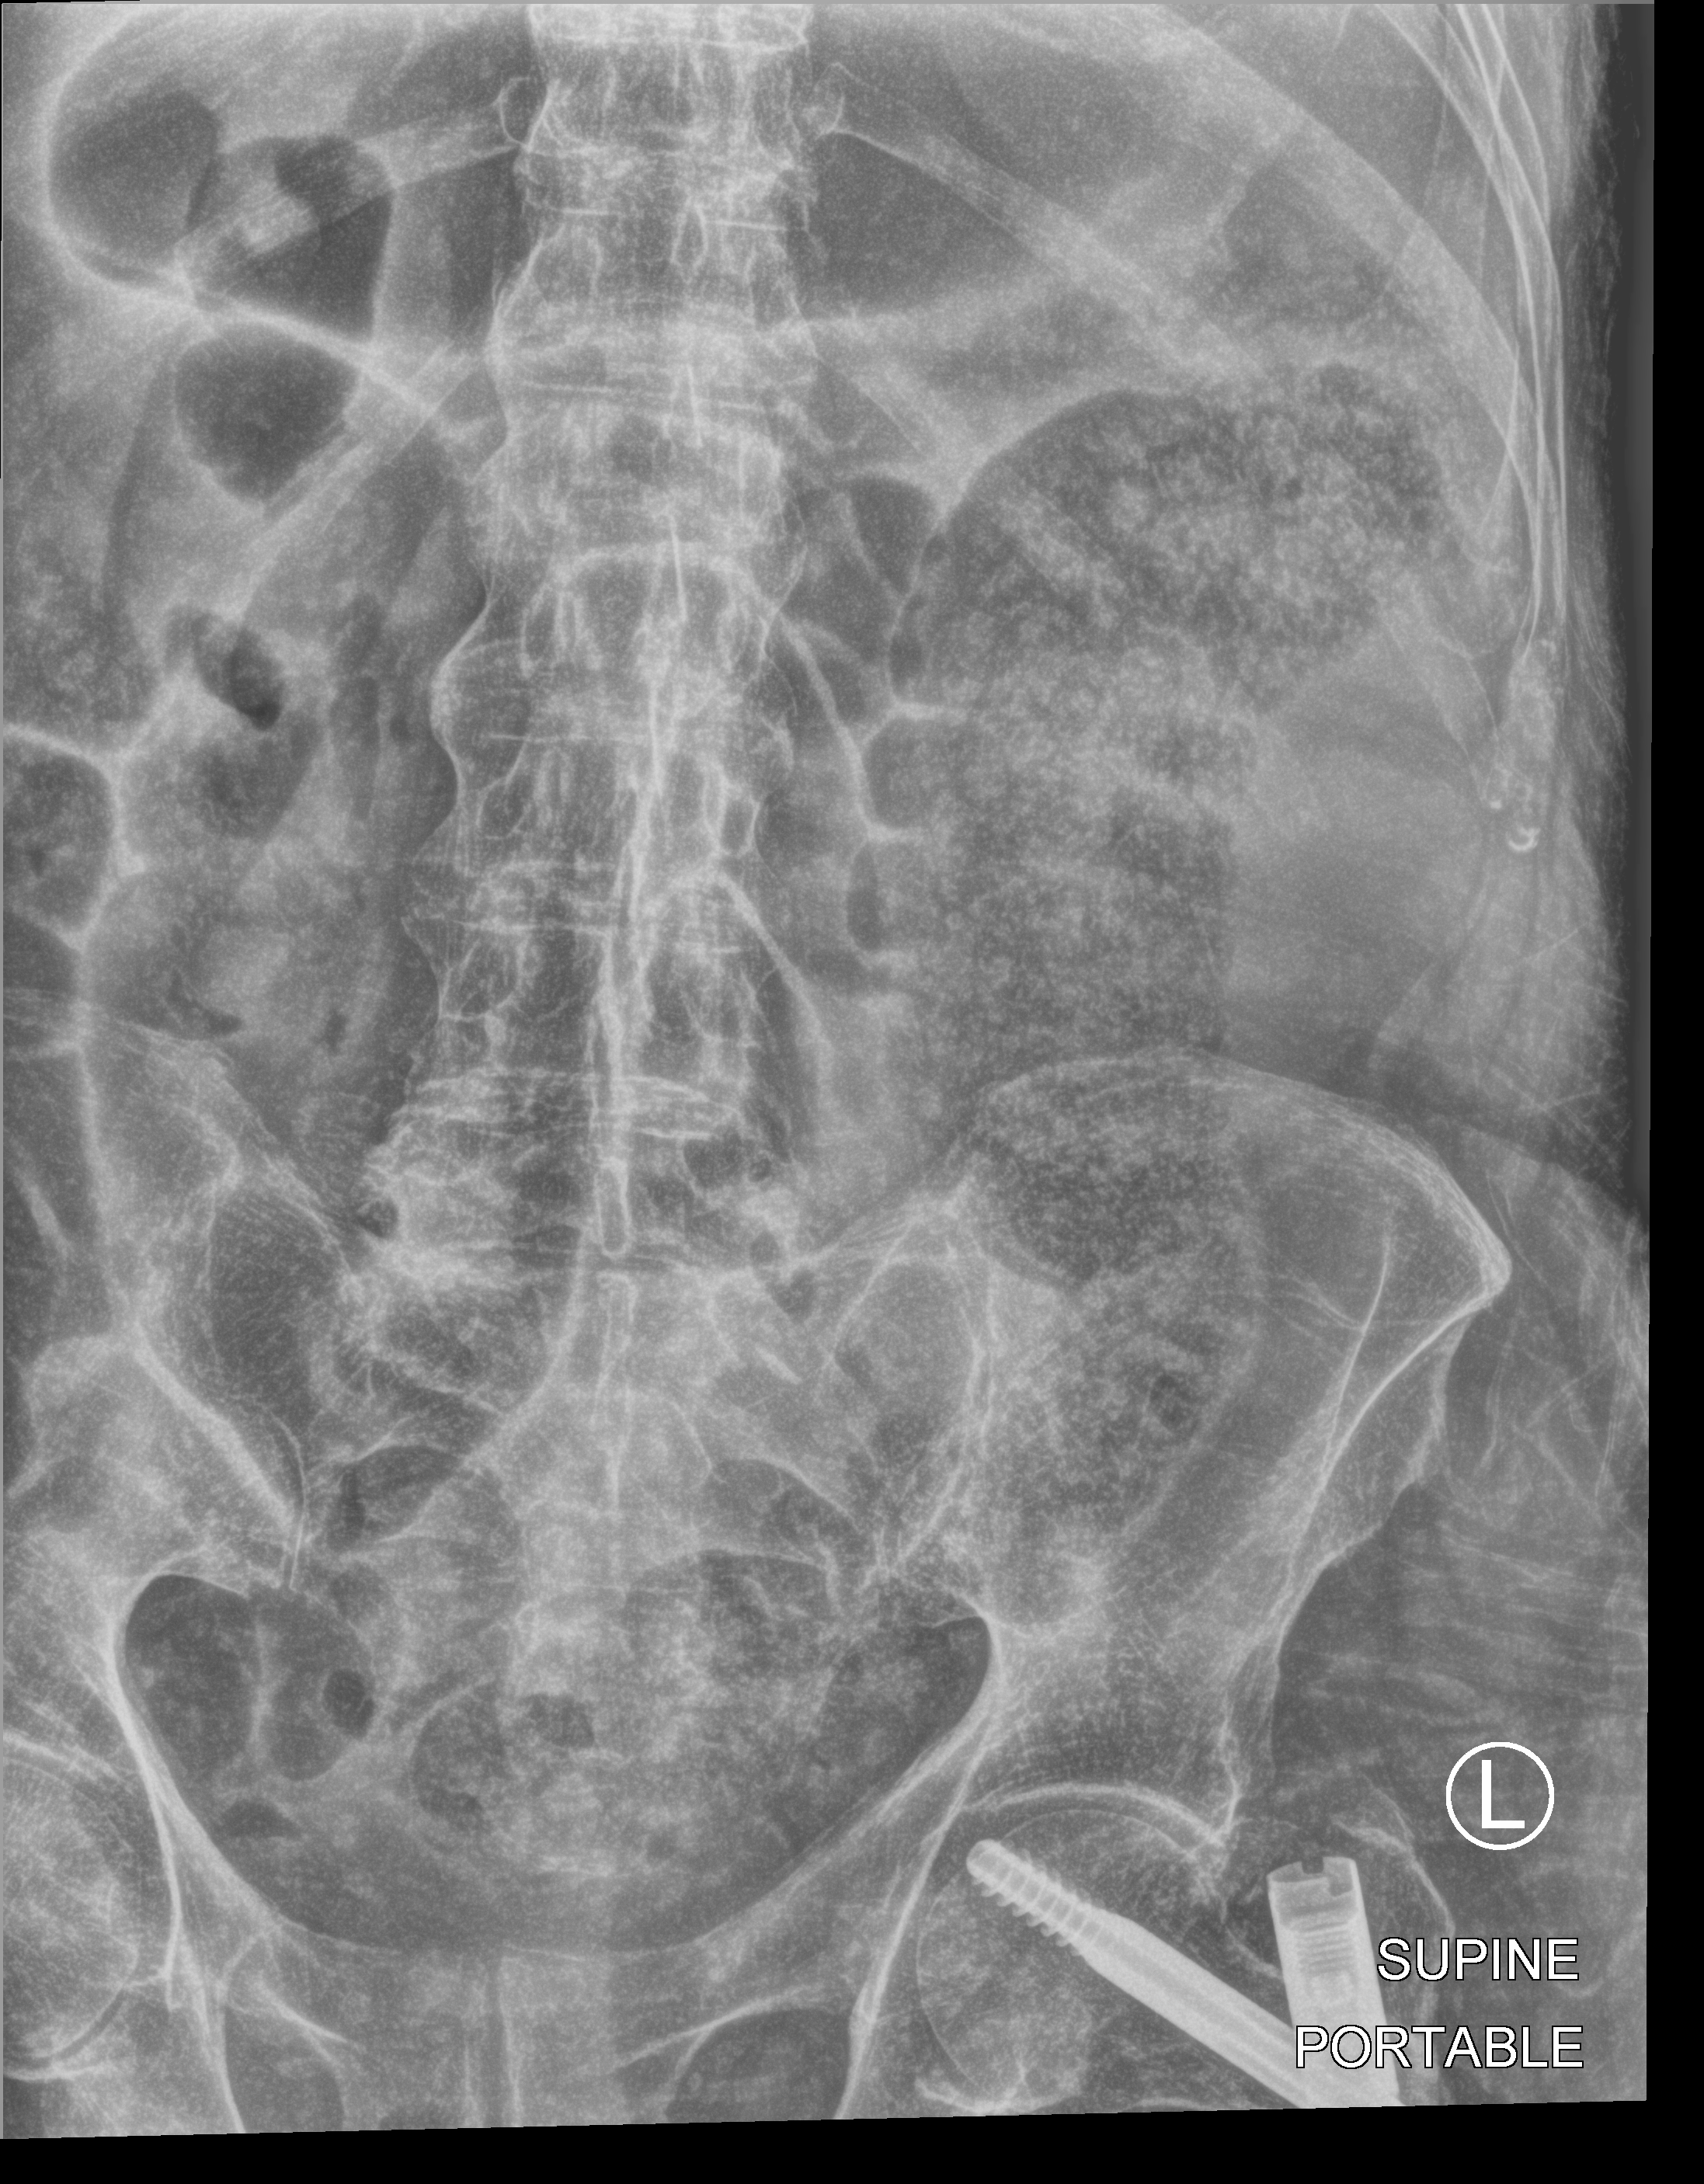
Bedside abdomen radiograph (computed radiography); anteroposterior (AP) projection. Male patient hospitalised with COVID-19, age 75–90 years.
Admission-level facts for this patient (not findings on this image; timing relative to this image not recorded): admitted to intensive care during this hospital stay: no; mechanically ventilated during this hospital stay: no.